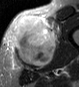
MRI of an extremity soft-tissue mass, one axial slice; slice 21 of 45 in the series (ordered by position); STIR; MR volume resampled by the dataset authors to the PET/CT grid (not the native acquisition matrix); 3.27 mm slice thickness; 79 × 87 image matrix, field of view 77 × 85 mm. Male patient. Case-level facts recorded for this patient, not image findings: histological type: pleiomorphic leiomyosarcoma; grade: high; site of the primary tumour: left thigh.
Structures marked on this image (expert contour drawn on MRI and transferred to this co-registered scan by the dataset authors):
- gross tumour volume including surrounding oedema: bounding box <11,16,60,67> (left, top, right, bottom; pixels)
- gross tumour volume (mass): <11,16,55,67>